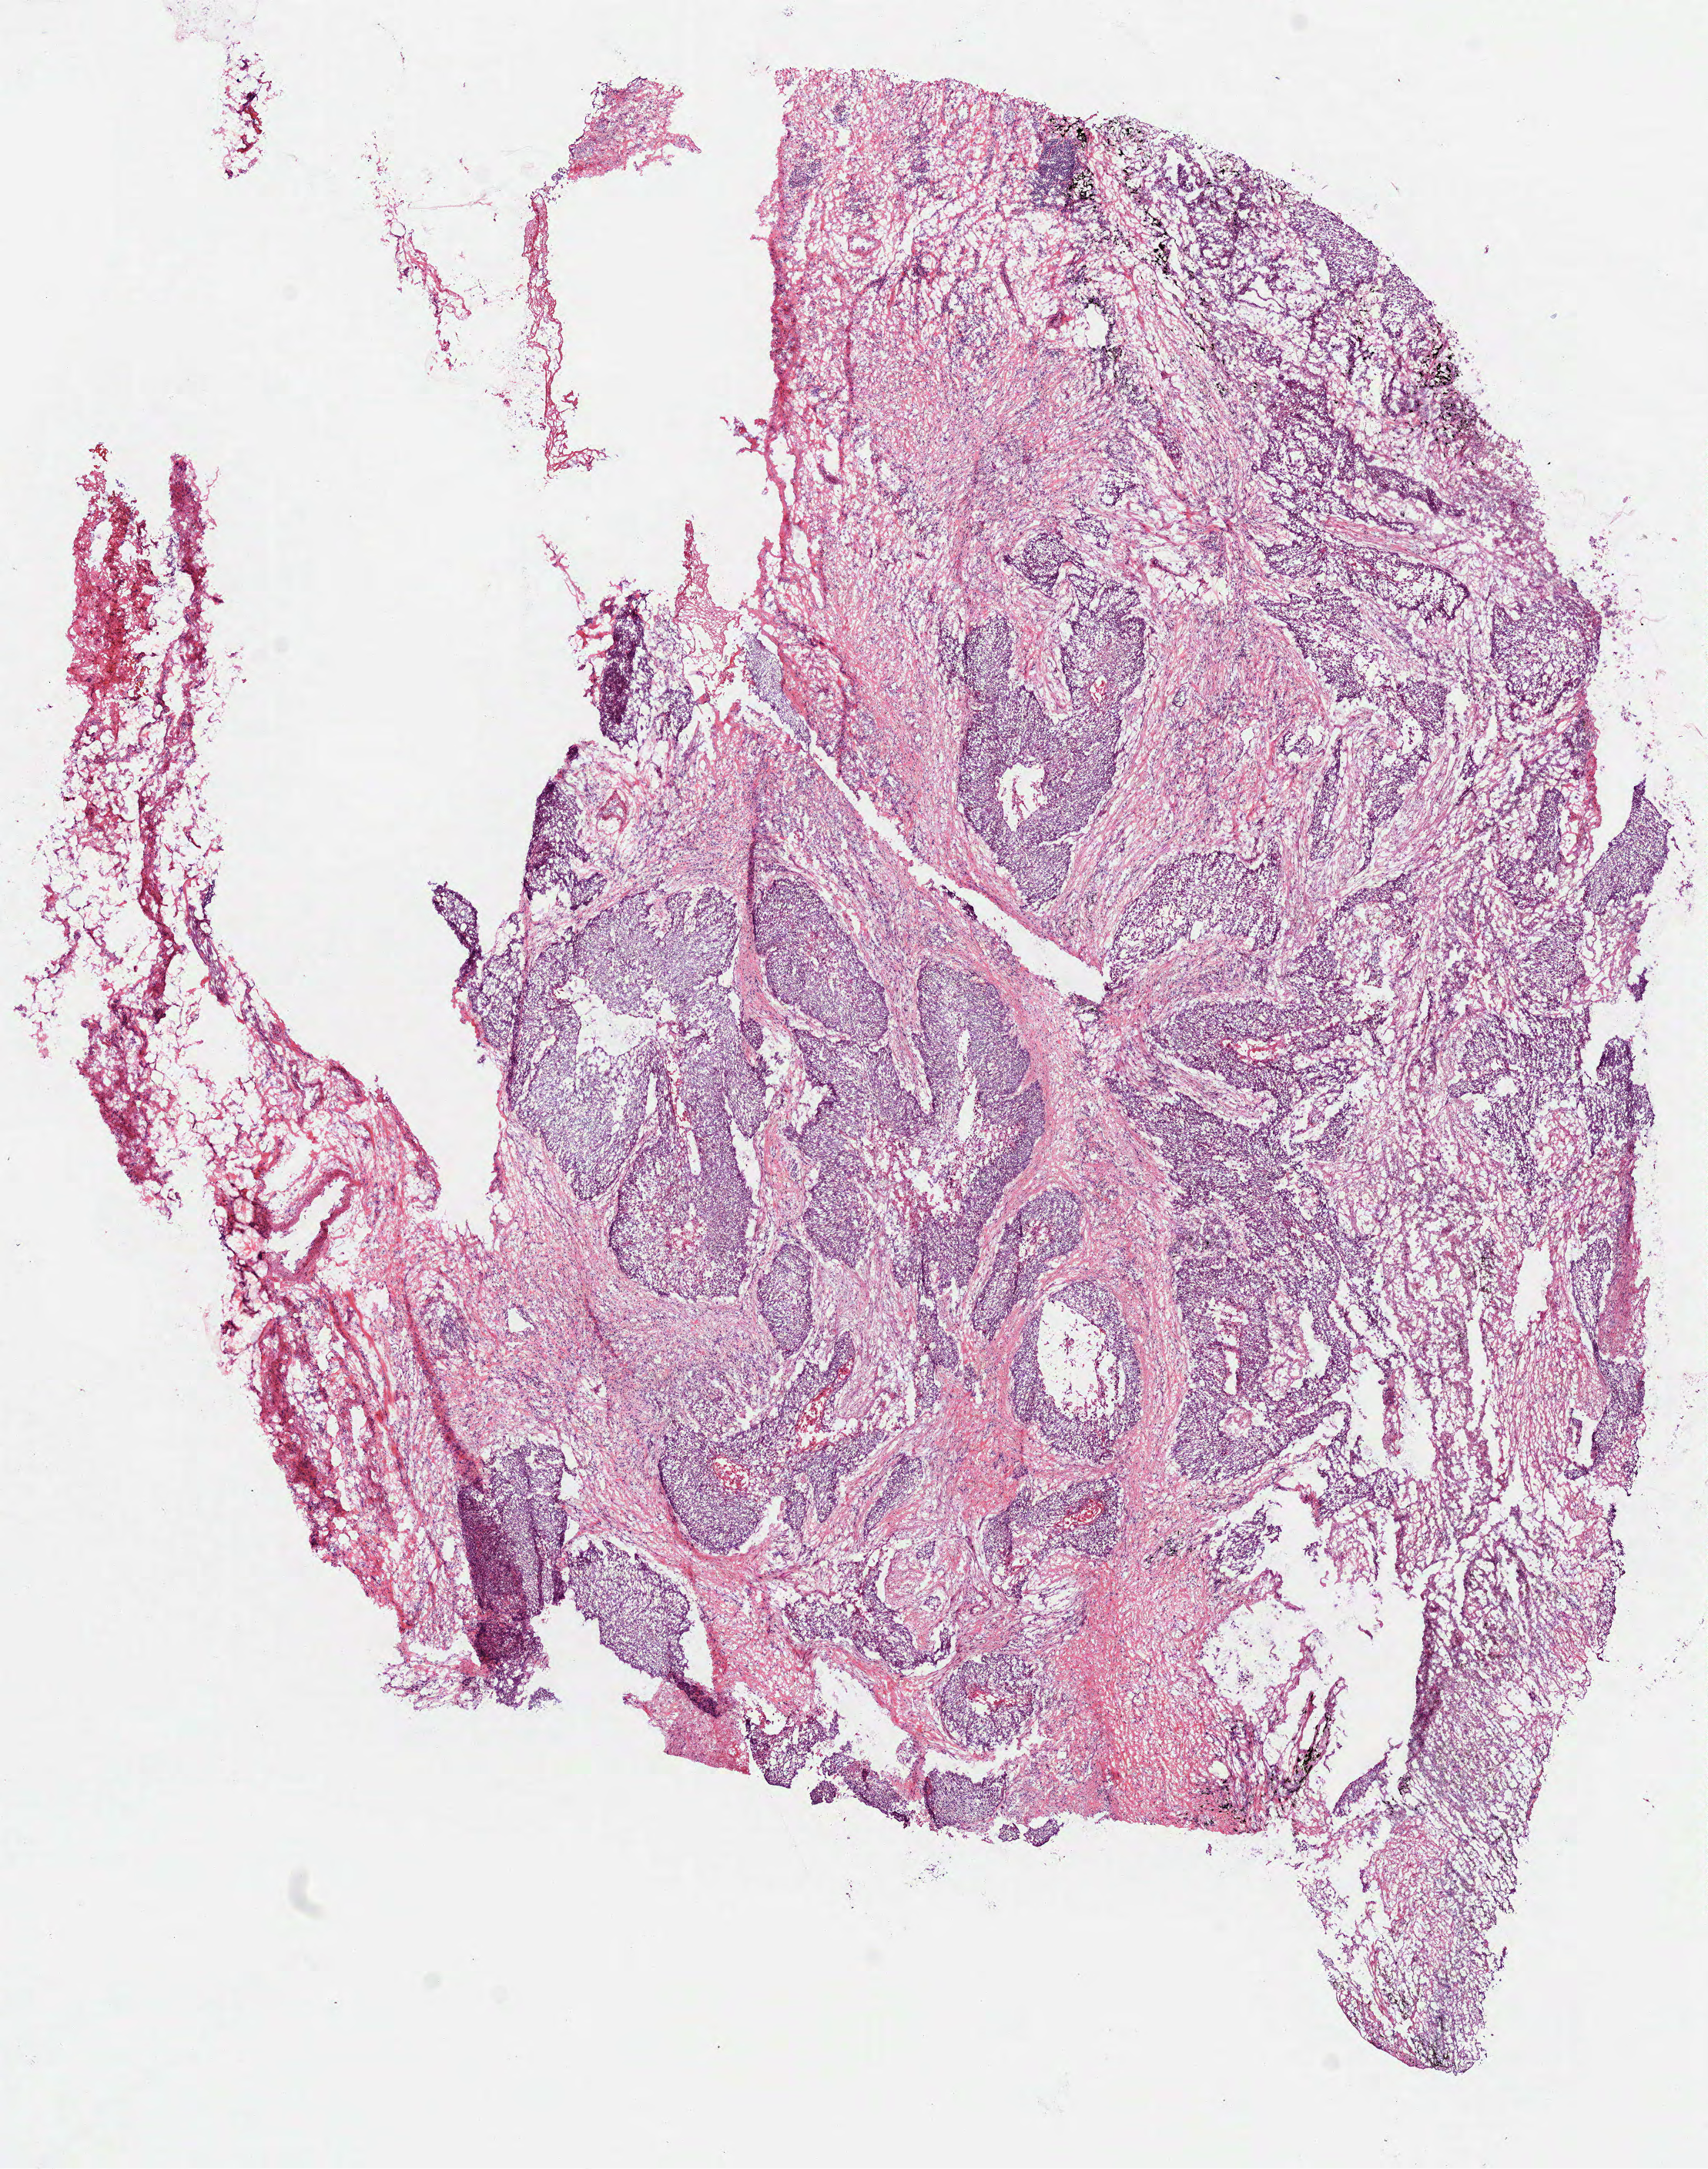
Digitized Hematoxylin and eosin (H&E) stained tissue section (whole slide) — whole scanned area (about 8.9 x 11.4 mm, slide scanned at 40x) shown as a low-resolution overview; frozen section from the top of the tissue portion; lung, primary tumour sample. Patient: male, age at initial diagnosis 70 years. Slide review estimates, as recorded: tumour cells 73%, tumour nuclei 70%, normal cells 0%, stromal cells 24%, necrosis 3%. Inflammatory infiltration, as recorded: lymphocyte infiltration 15%, monocyte infiltration 0%, neutrophil infiltration 2%.
• pathologic diagnosis: Squamous cell carcinoma, NOS (lower lobe, lung)
• AJCC pathologic stage: II